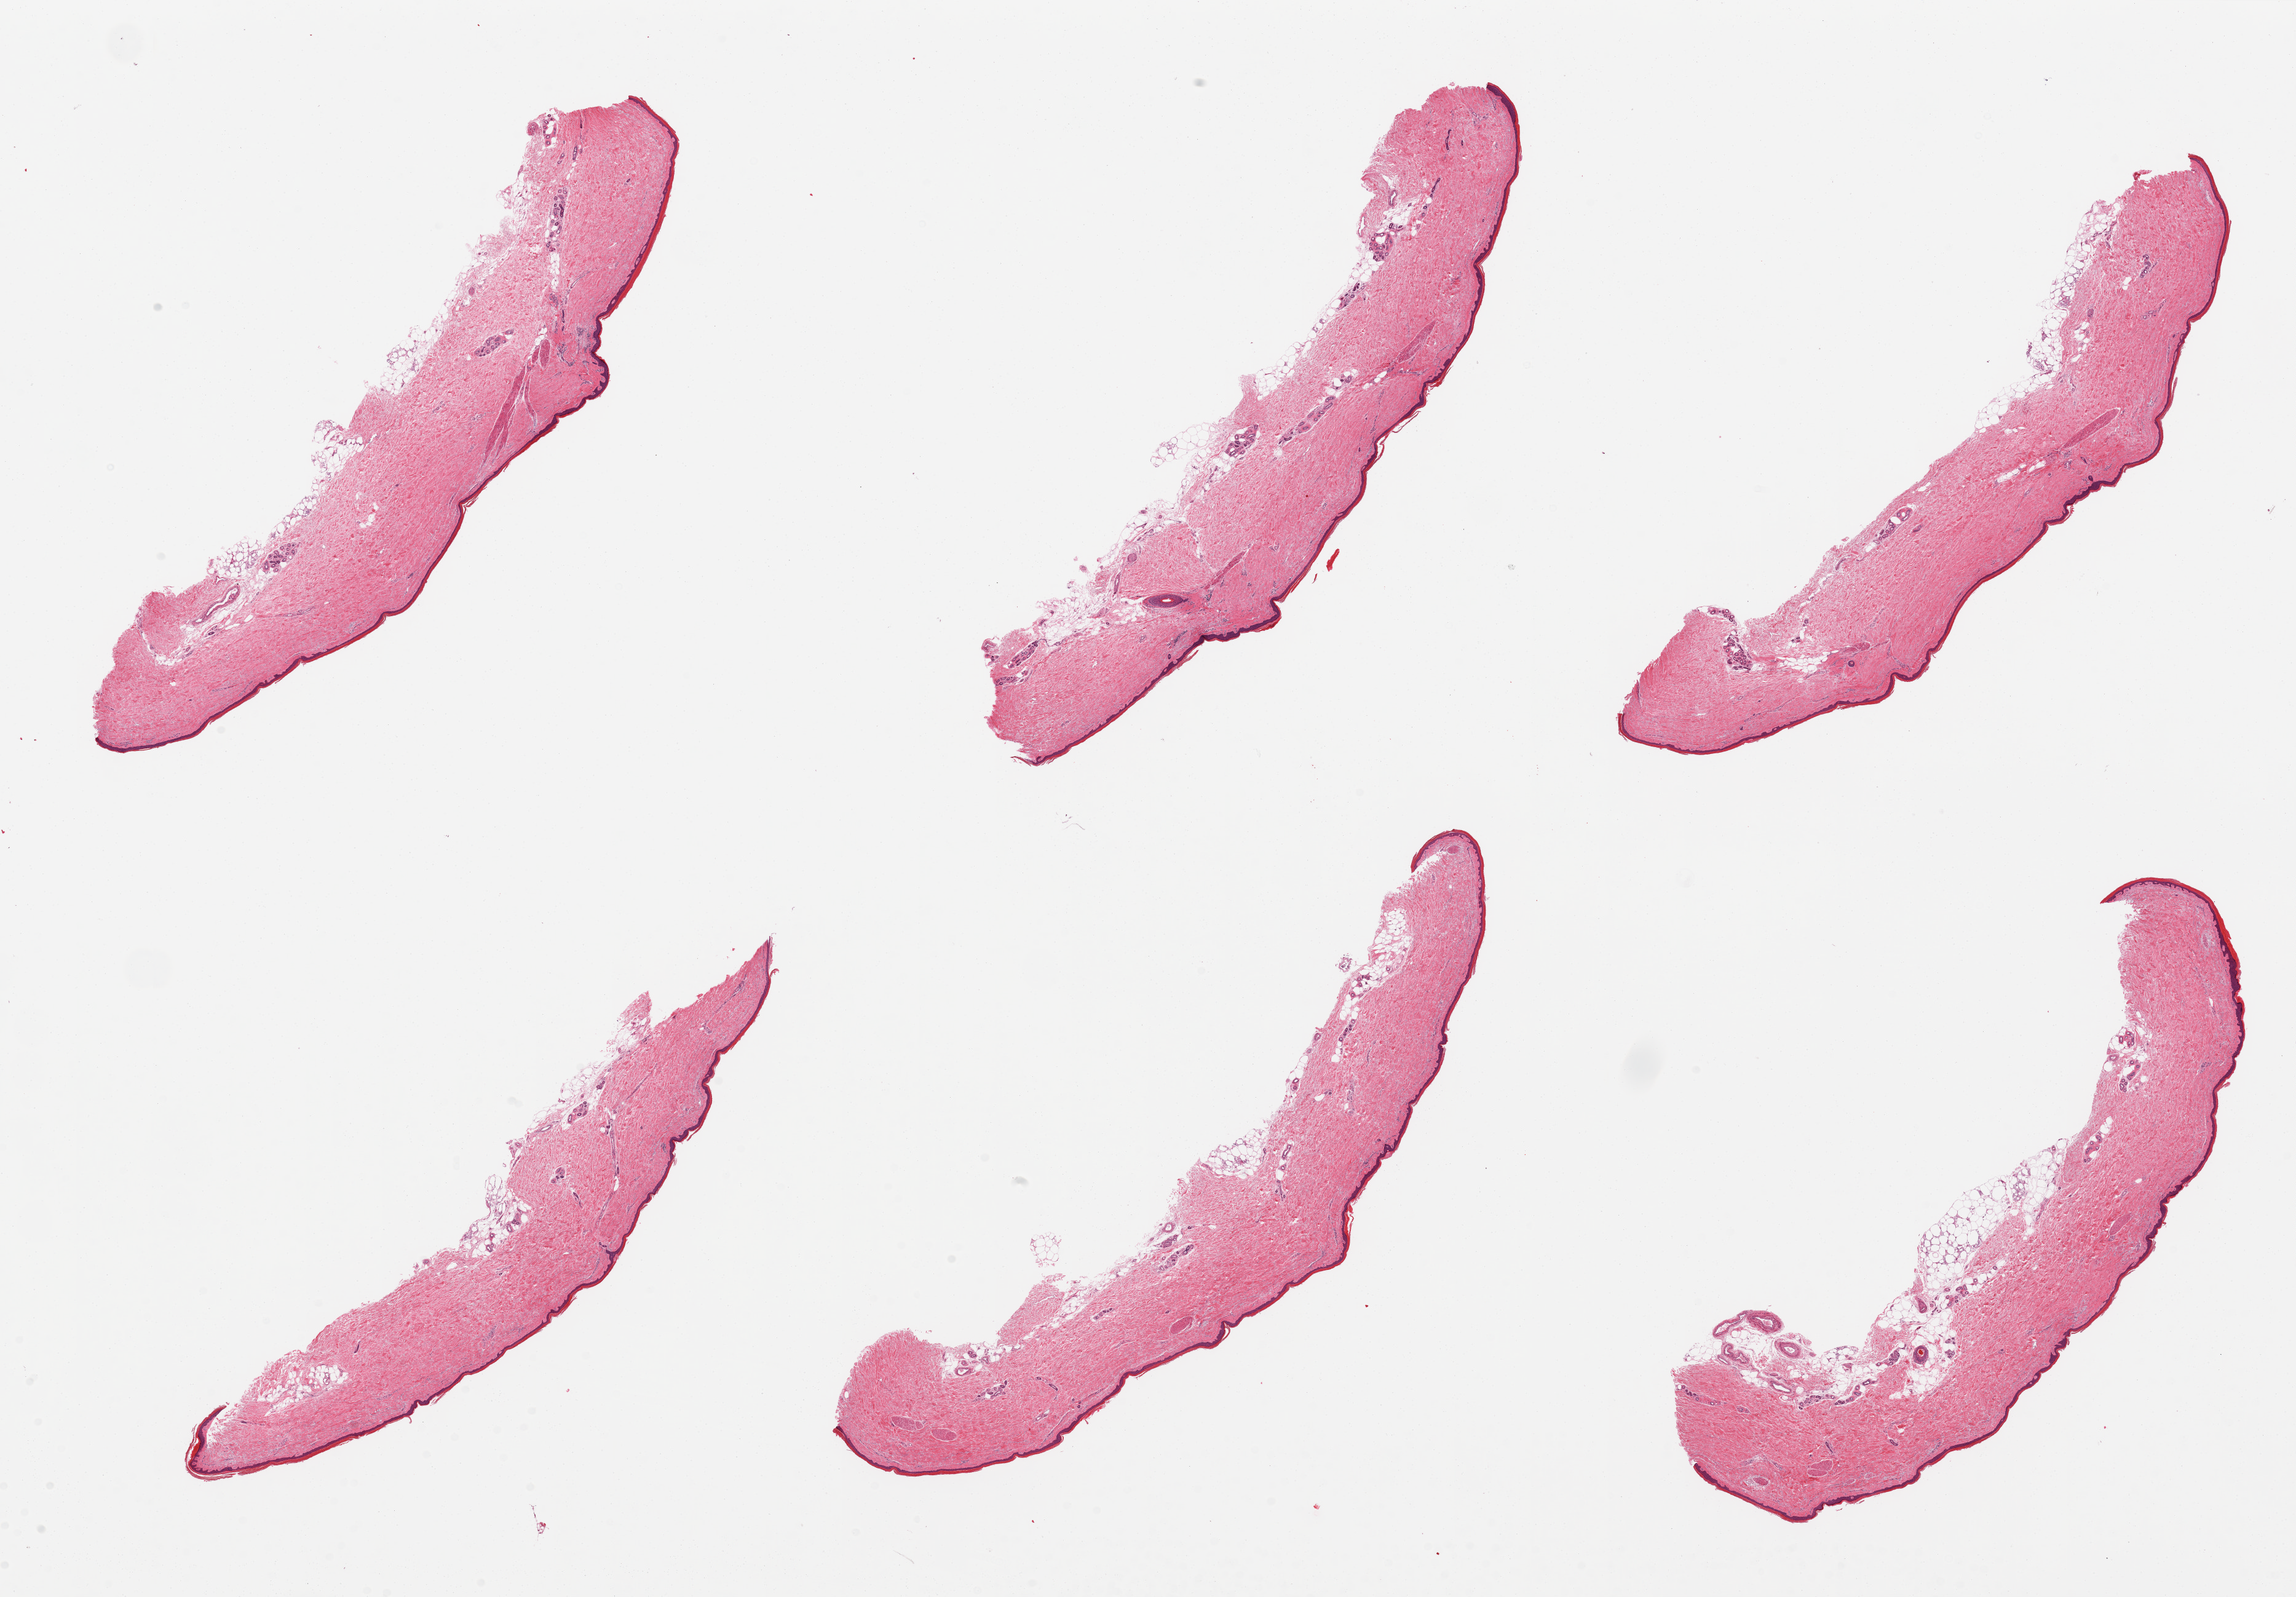
Whole-slide image, H&E stain, brightfield — a low-resolution overview of the entire scanned area, about 29.5 x 20.5 mm (acquisition: 20x scan), PAXgene-fixed paraffin-embedded (PFPE) section, sampled site (target tissue): skin of lower leg, donor tissue sample. Male donor.
• review note (as recorded): 6 pieces; well trimmed